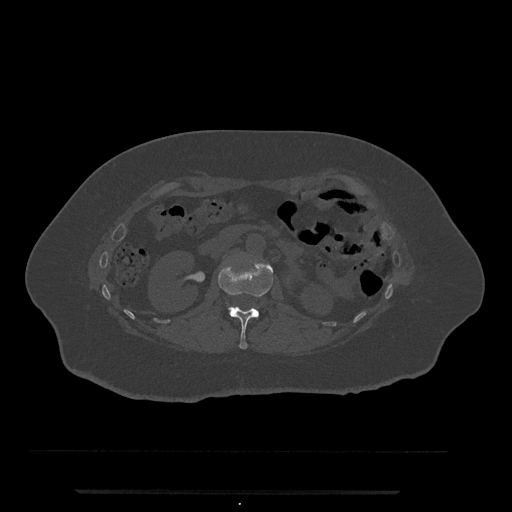
CT including the spine, one axial slice; 120 kVp; bone window (W 1800 / L 400 HU); 512 × 512 image matrix. Patient: female, 51 years. Case-level facts recorded for this patient, not image findings: primary cancer: neuro; vertebrae with lytic lesions (as recorded): T8.
Outlined on this slice (semi-automatically segmented with operator editing):
- L1 vertebra: bounding box [x1, y1, x2, y2] px = [218, 255, 274, 349]
- L2 vertebra: [228, 306, 234, 311]